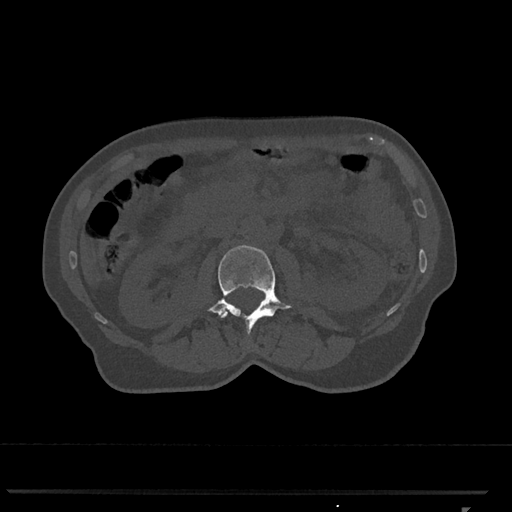
CT including the spine, one axial slice; position 339 of 793 along the scan axis; reconstruction kernel Br40s/3; 120 kVp; bone window (W 1800 / L 400 HU); 0.5 mm slice thickness; 512 × 512 image matrix. Female patient, age 62 years. Case-level facts recorded for this patient, not image findings: primary cancer: renal.
Structures marked on this image (semi-automatic segmentation, software-assisted and operator-edited):
- L2 vertebra: box from (x=207, y=245) to (x=292, y=334) px